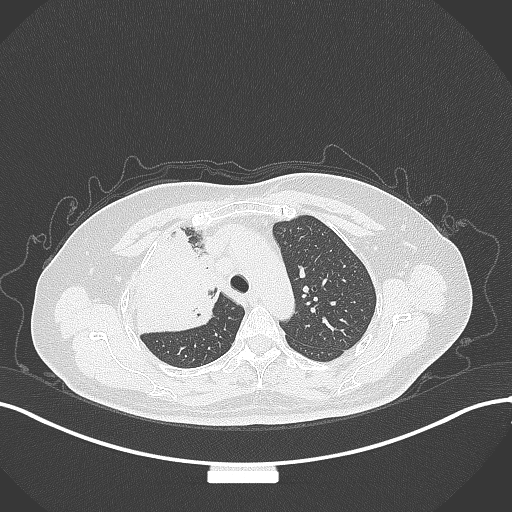
Chest CT, one axial slice; position 232 of 309 along the scan axis; reconstruction kernel B70f; 120 kVp; lung window (W 1500 / L -600 HU); 1 mm slice thickness; 512 × 512 image matrix, field of view 400 × 400 mm. Female patient, age 60 years. Case-level facts recorded for this patient, not image findings: clinical TNM (as recorded): T3 N1 M1.
Outlined on this slice (bounding box drawn by a radiologist):
- lung tumour (recorded histology: adenocarcinoma): bounding box <130,230,222,342> (left, top, right, bottom; pixels)